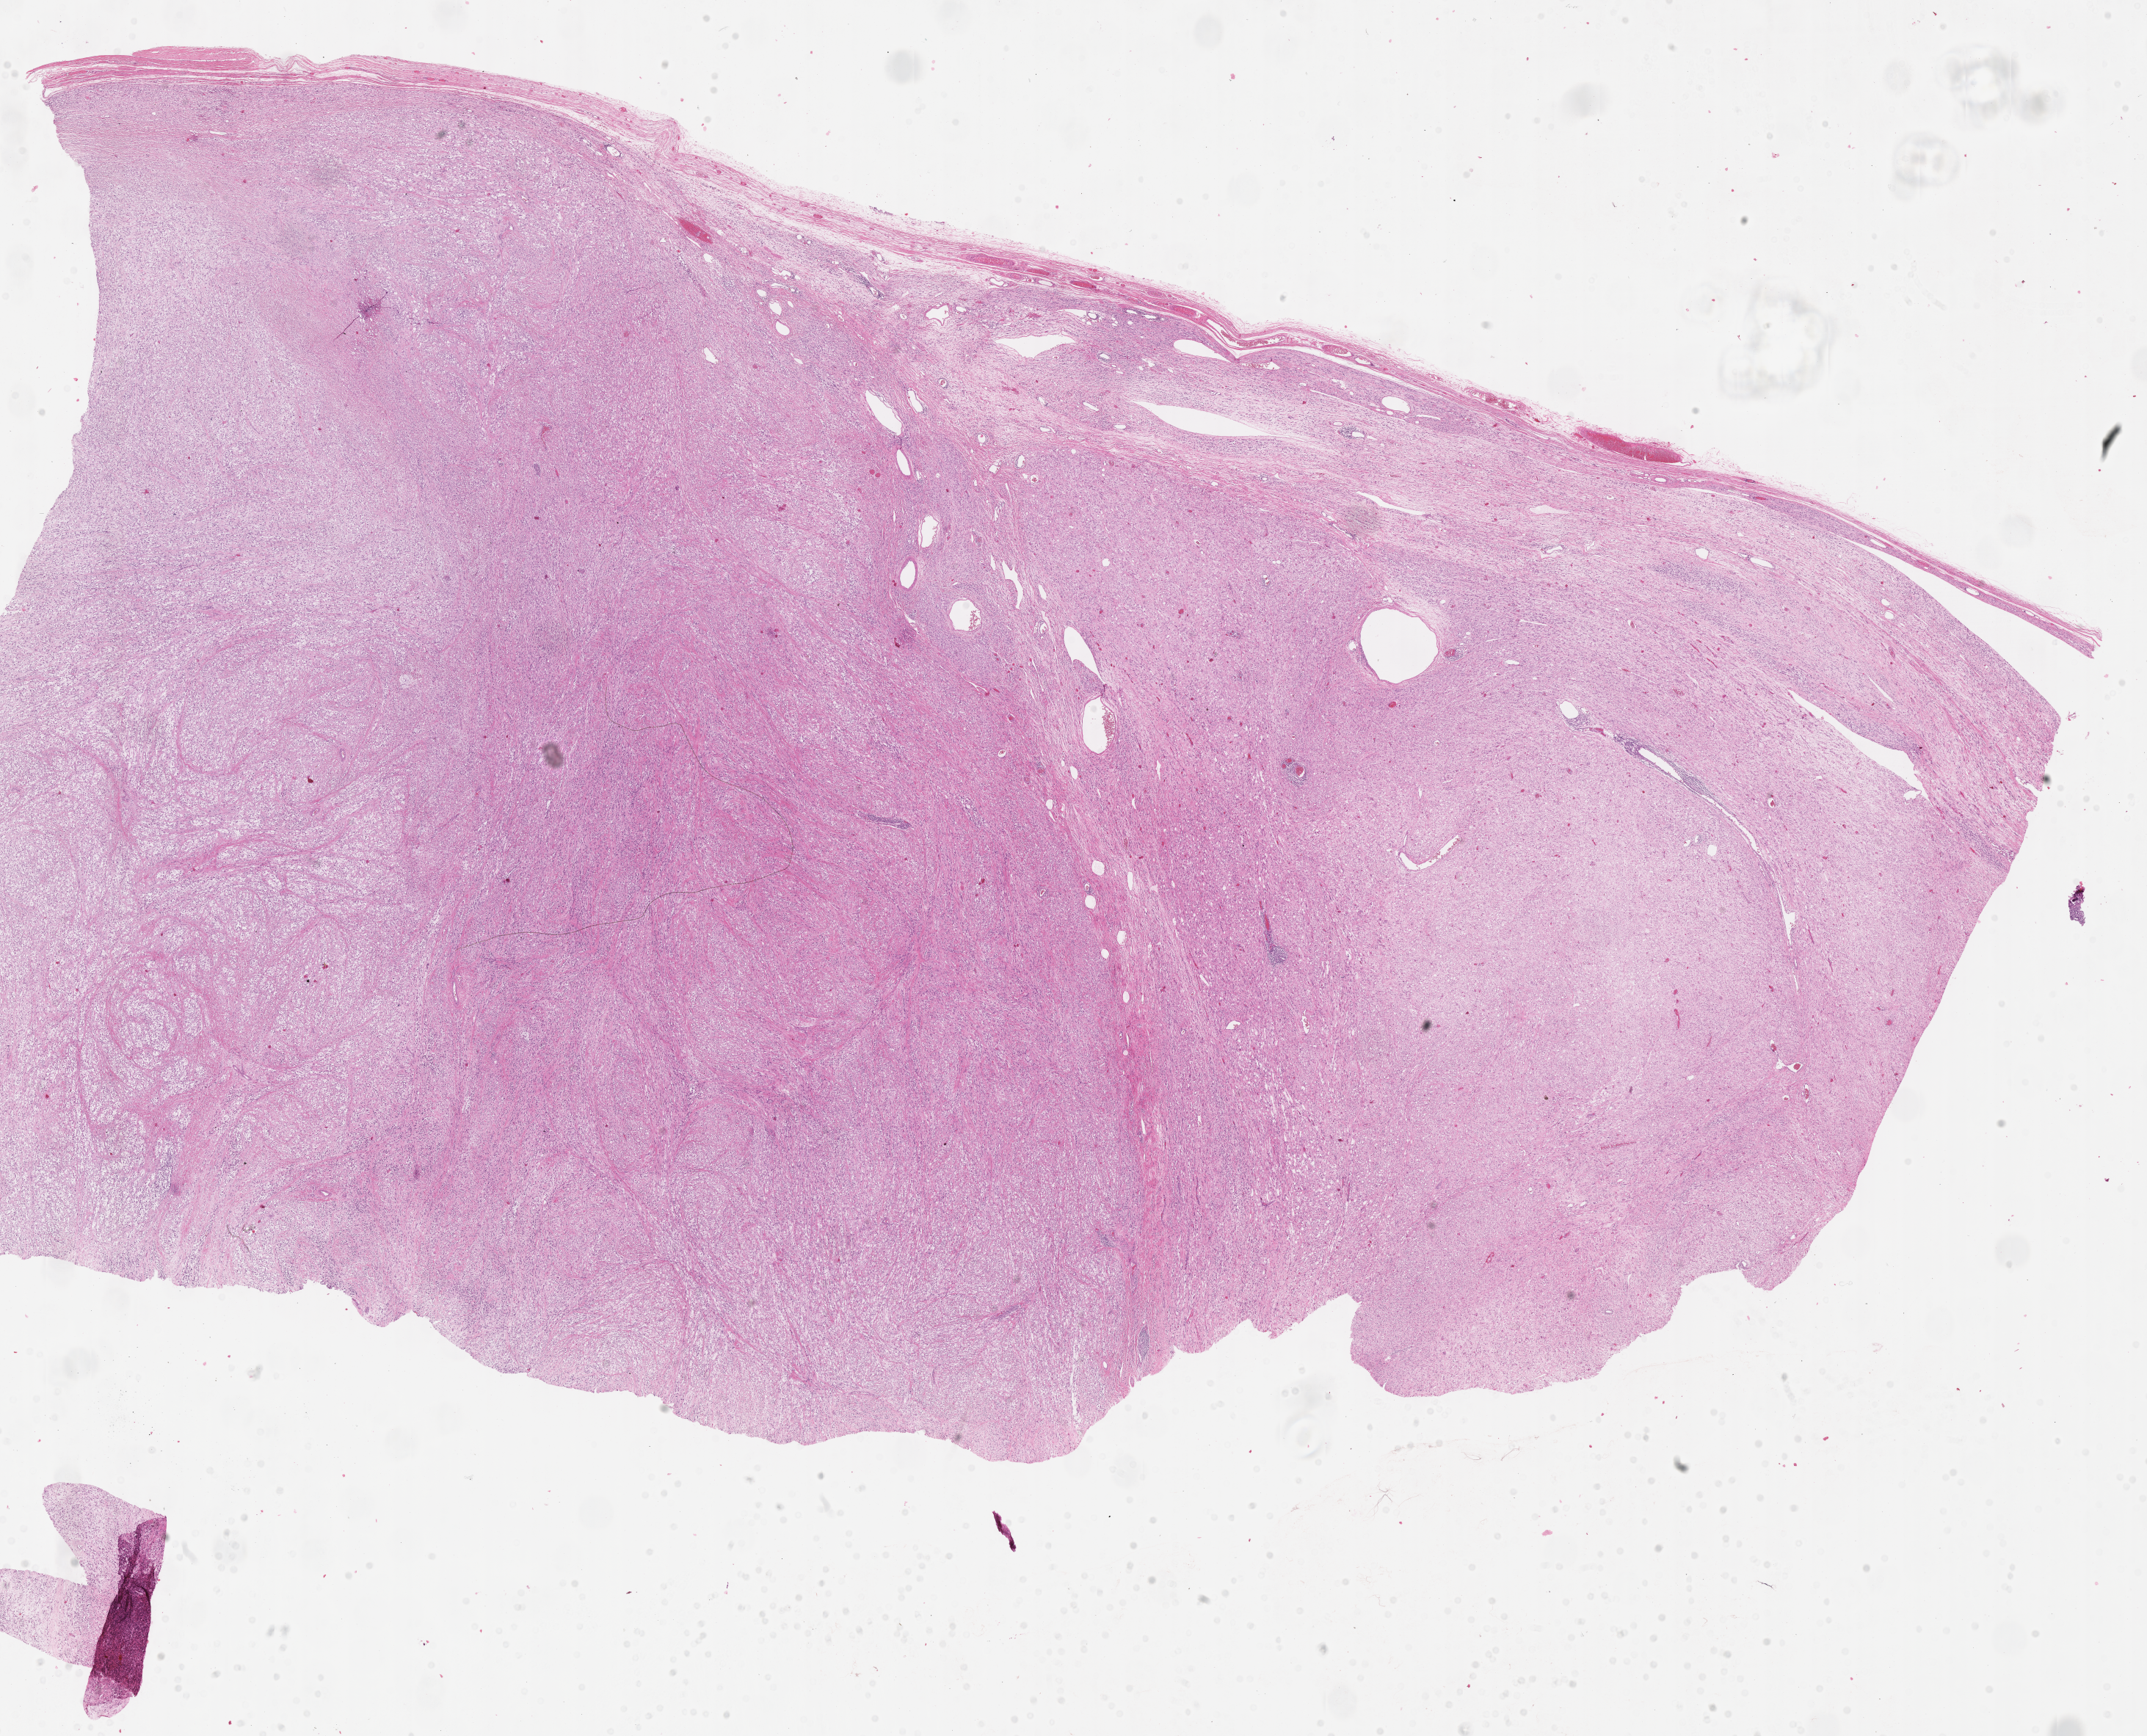
Whole-slide image, haematoxylin and eosin stain of tumor tissue — whole scanned area (about 23.6 x 19.1 mm) shown as a low-resolution overview; formalin-fixed paraffin-embedded section; sample anatomic site: testicle, right. Patient: male, age 16.7 years at diagnosis.
• stage (as recorded): 1
• primary site (case record): testis-Paratestis
• metastatic status at presentation (as recorded): non-metastatic
• diagnosis: rhabdomyosarcoma; histological classification: embryonal rhabdomyosarcoma